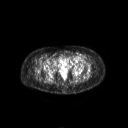
FDG PET of an extremity soft-tissue mass (from a PET/CT study), one axial slice; slice 52 of 267 in the series (ordered by position); 3.27 mm slice thickness; 128 × 128 image matrix, field of view 700 × 700 mm. Female patient, age 47 years. Case-level facts recorded for this patient, not image findings: histological type: myxofibrosarcoma; grade: intermediate; site of the primary tumour: left thigh.
Annotated regions visible in this slice (expert contour drawn on MRI and transferred to this co-registered scan by the dataset authors):
- gross tumour volume including surrounding oedema: bounding box <66,57,82,63> (left, top, right, bottom; pixels)